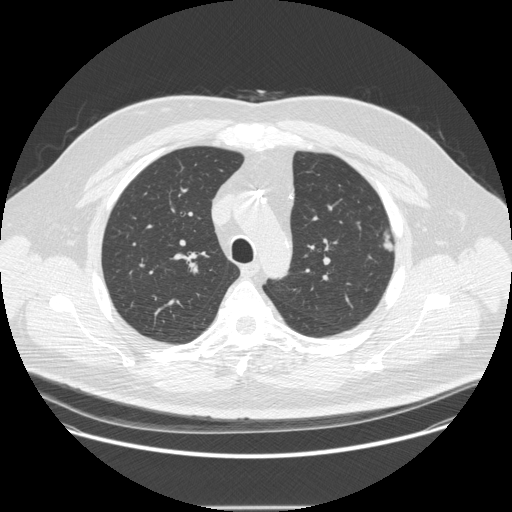
Chest CT (low-dose screening protocol), one axial image. Second screening round (one year after baseline). Lung window (W 1500 / L -600 HU). 1.25 mm slice thickness. 120 kVp. Slice 74 of 251 in the series. 512 × 512 image matrix. Male, age 55 years at enrolment.
• Expert-annotated lung lesion, box from (x=373, y=228) to (x=405, y=251) px.
• The screening reader recorded 2 non-calcified nodules or masses ≥4 mm on this exam (left upper lobe, left upper lobe); which of them this box marks is not recorded.
• Official screen result: positive, other.
• Later outcome: lung cancer diagnosed 60 days after this screen — adenocarcinoma, NOS, left upper lobe, moderately differentiated (G2), stage IA (AJCC 6th edition), 9 mm at pathology.